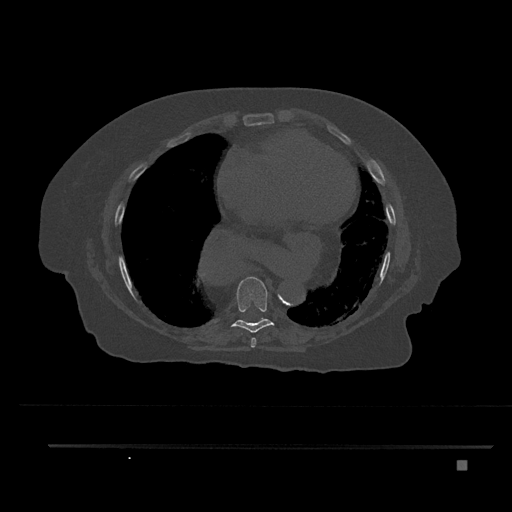
CT including the spine, one axial slice. Reconstruction kernel Br40s/3. 120 kVp. Bone window (W 1800 / L 400 HU). 512 × 512 image matrix, field of view 437 × 437 mm. Female patient, age 76 years. Case-level facts recorded for this patient, not image findings: primary cancer: lung; vertebrae with lytic lesions (as recorded): T11, L3.
Outlined on this slice (semi-automatic segmentation, software-assisted and operator-edited):
- T7 vertebra: bounding box [x1, y1, x2, y2] px = [250, 337, 256, 348]
- T8 vertebra: [231, 277, 275, 333]